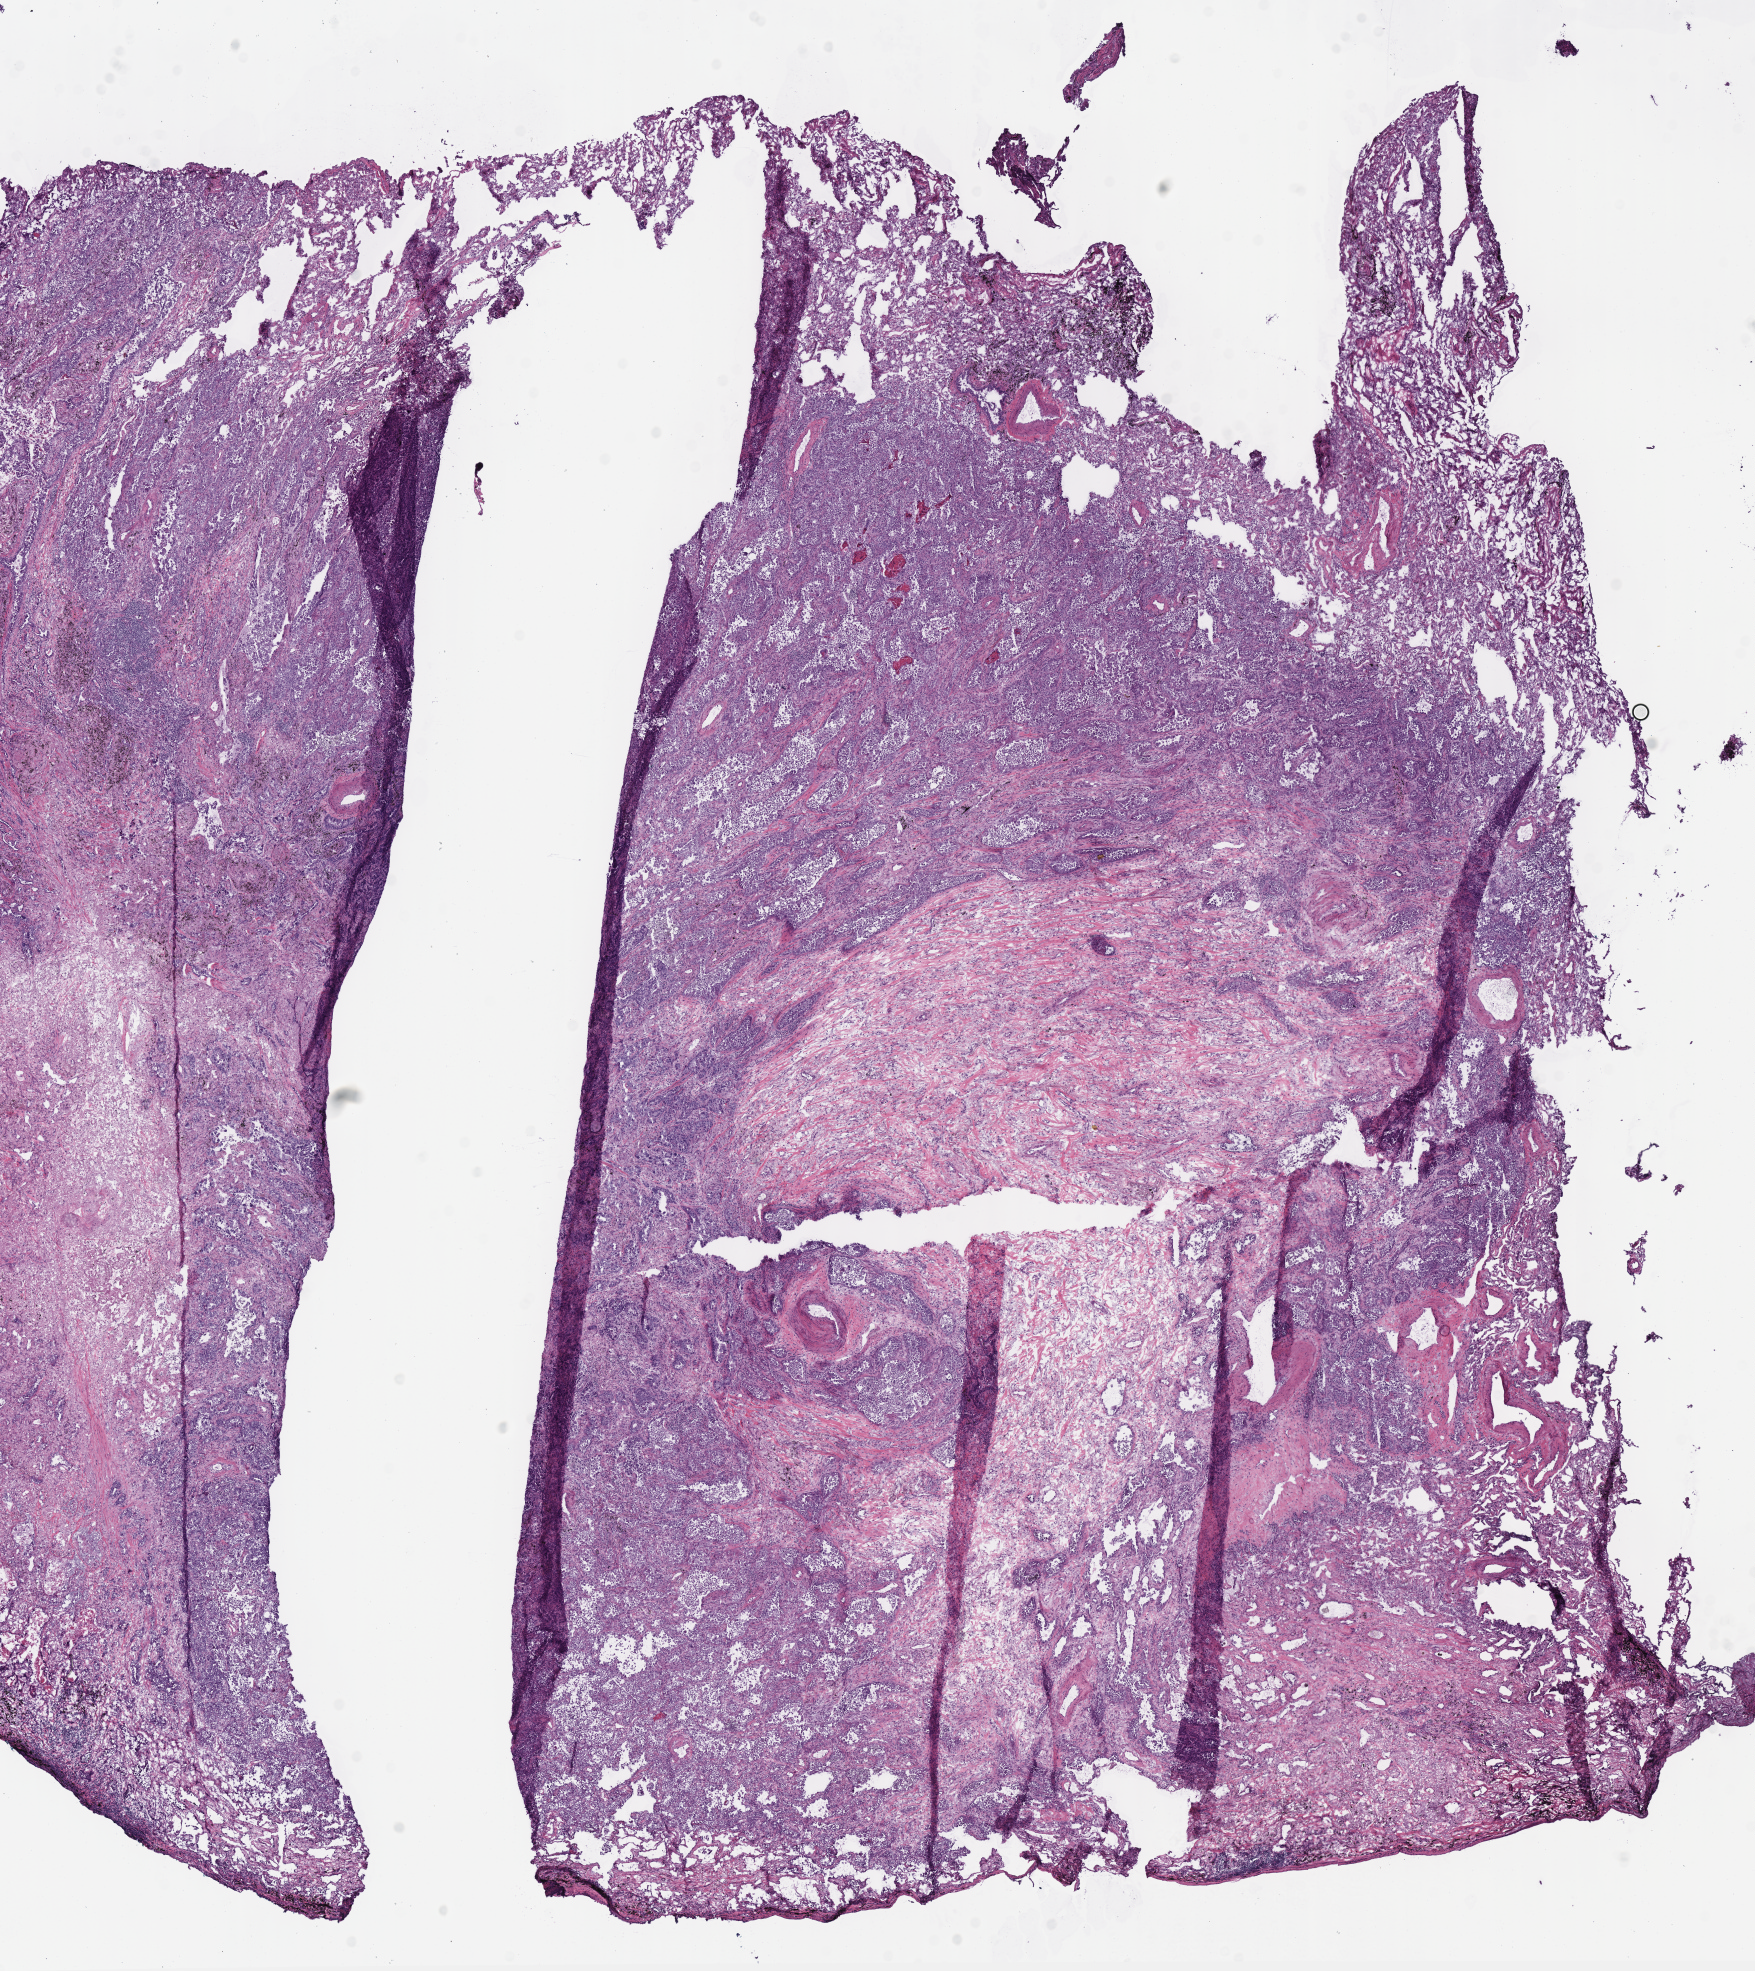
Whole-slide histology image, Hematoxylin and eosin (H&E) stained, shown as a low-resolution overview of the whole scanned area (about 13.8 x 15.5 mm, acquisition: 40x scan). Frozen section from the top of the tissue portion. Sample: primary tumour, lung. Patient: male, age at initial diagnosis 58 years. Pathologist review of this section (percent, as recorded): tumour cells 74%, tumour nuclei 80%, normal cells 8%, stromal cells 16%, necrosis 2%. Infiltration values recorded for this section: lymphocyte infiltration 10%, monocyte infiltration 2%, neutrophil infiltration 2%.
• AJCC pathologic stage: IB
• diagnosis: Bronchiolo-alveolar adenocarcinoma, NOS (upper lobe, lung)